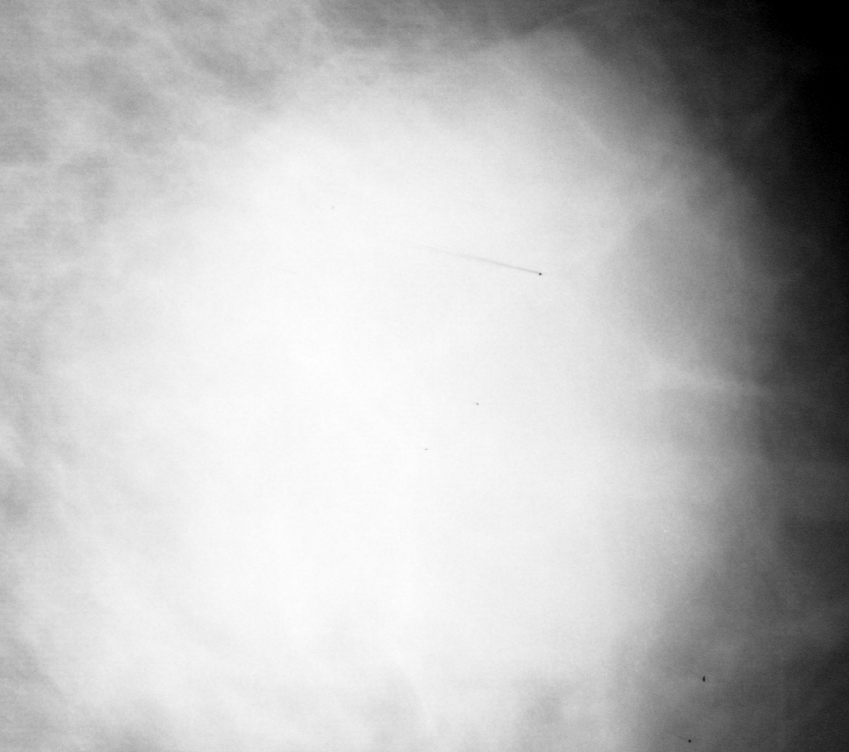
Crop from a digitized film mammogram around one marked abnormality; left breast; MLO view; BI-RADS breast density category 2 (scale 1–4).
Mass, shape oval, margins microlobulated; BI-RADS assessment category 5; pathology (as recorded): malignant.